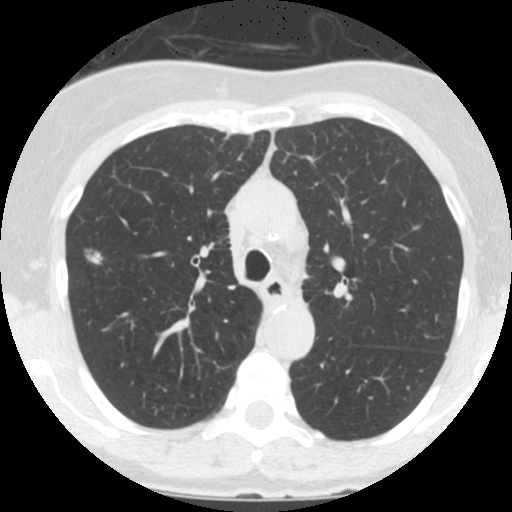
Low-dose screening chest CT, axial slice. Third screening round (two years after baseline). Lung window (W 1500 / L -600 HU). 2.5 mm slice thickness. 120 kVp. Female, age 60 years at enrolment.
- Expert-annotated lung lesion, bounding box <67,233,115,285> (left, top, right, bottom; pixels).
- Screening reader's record for this exam (one nodule recorded; not confirmed to be the boxed lesion): non-calcified nodule or mass ≥4 mm, right upper lobe, 12 × 12 mm, smooth margins, ground glass attenuation, pre-existing on the prior screen: yes; interval growth: yes.
- Lung cancer was diagnosed 56 days after this screen: bronchiolo-alveolar adenocarcinoma, NOS, right upper lobe, well differentiated (G1), stage IA (AJCC 6th edition), 11 mm at pathology.